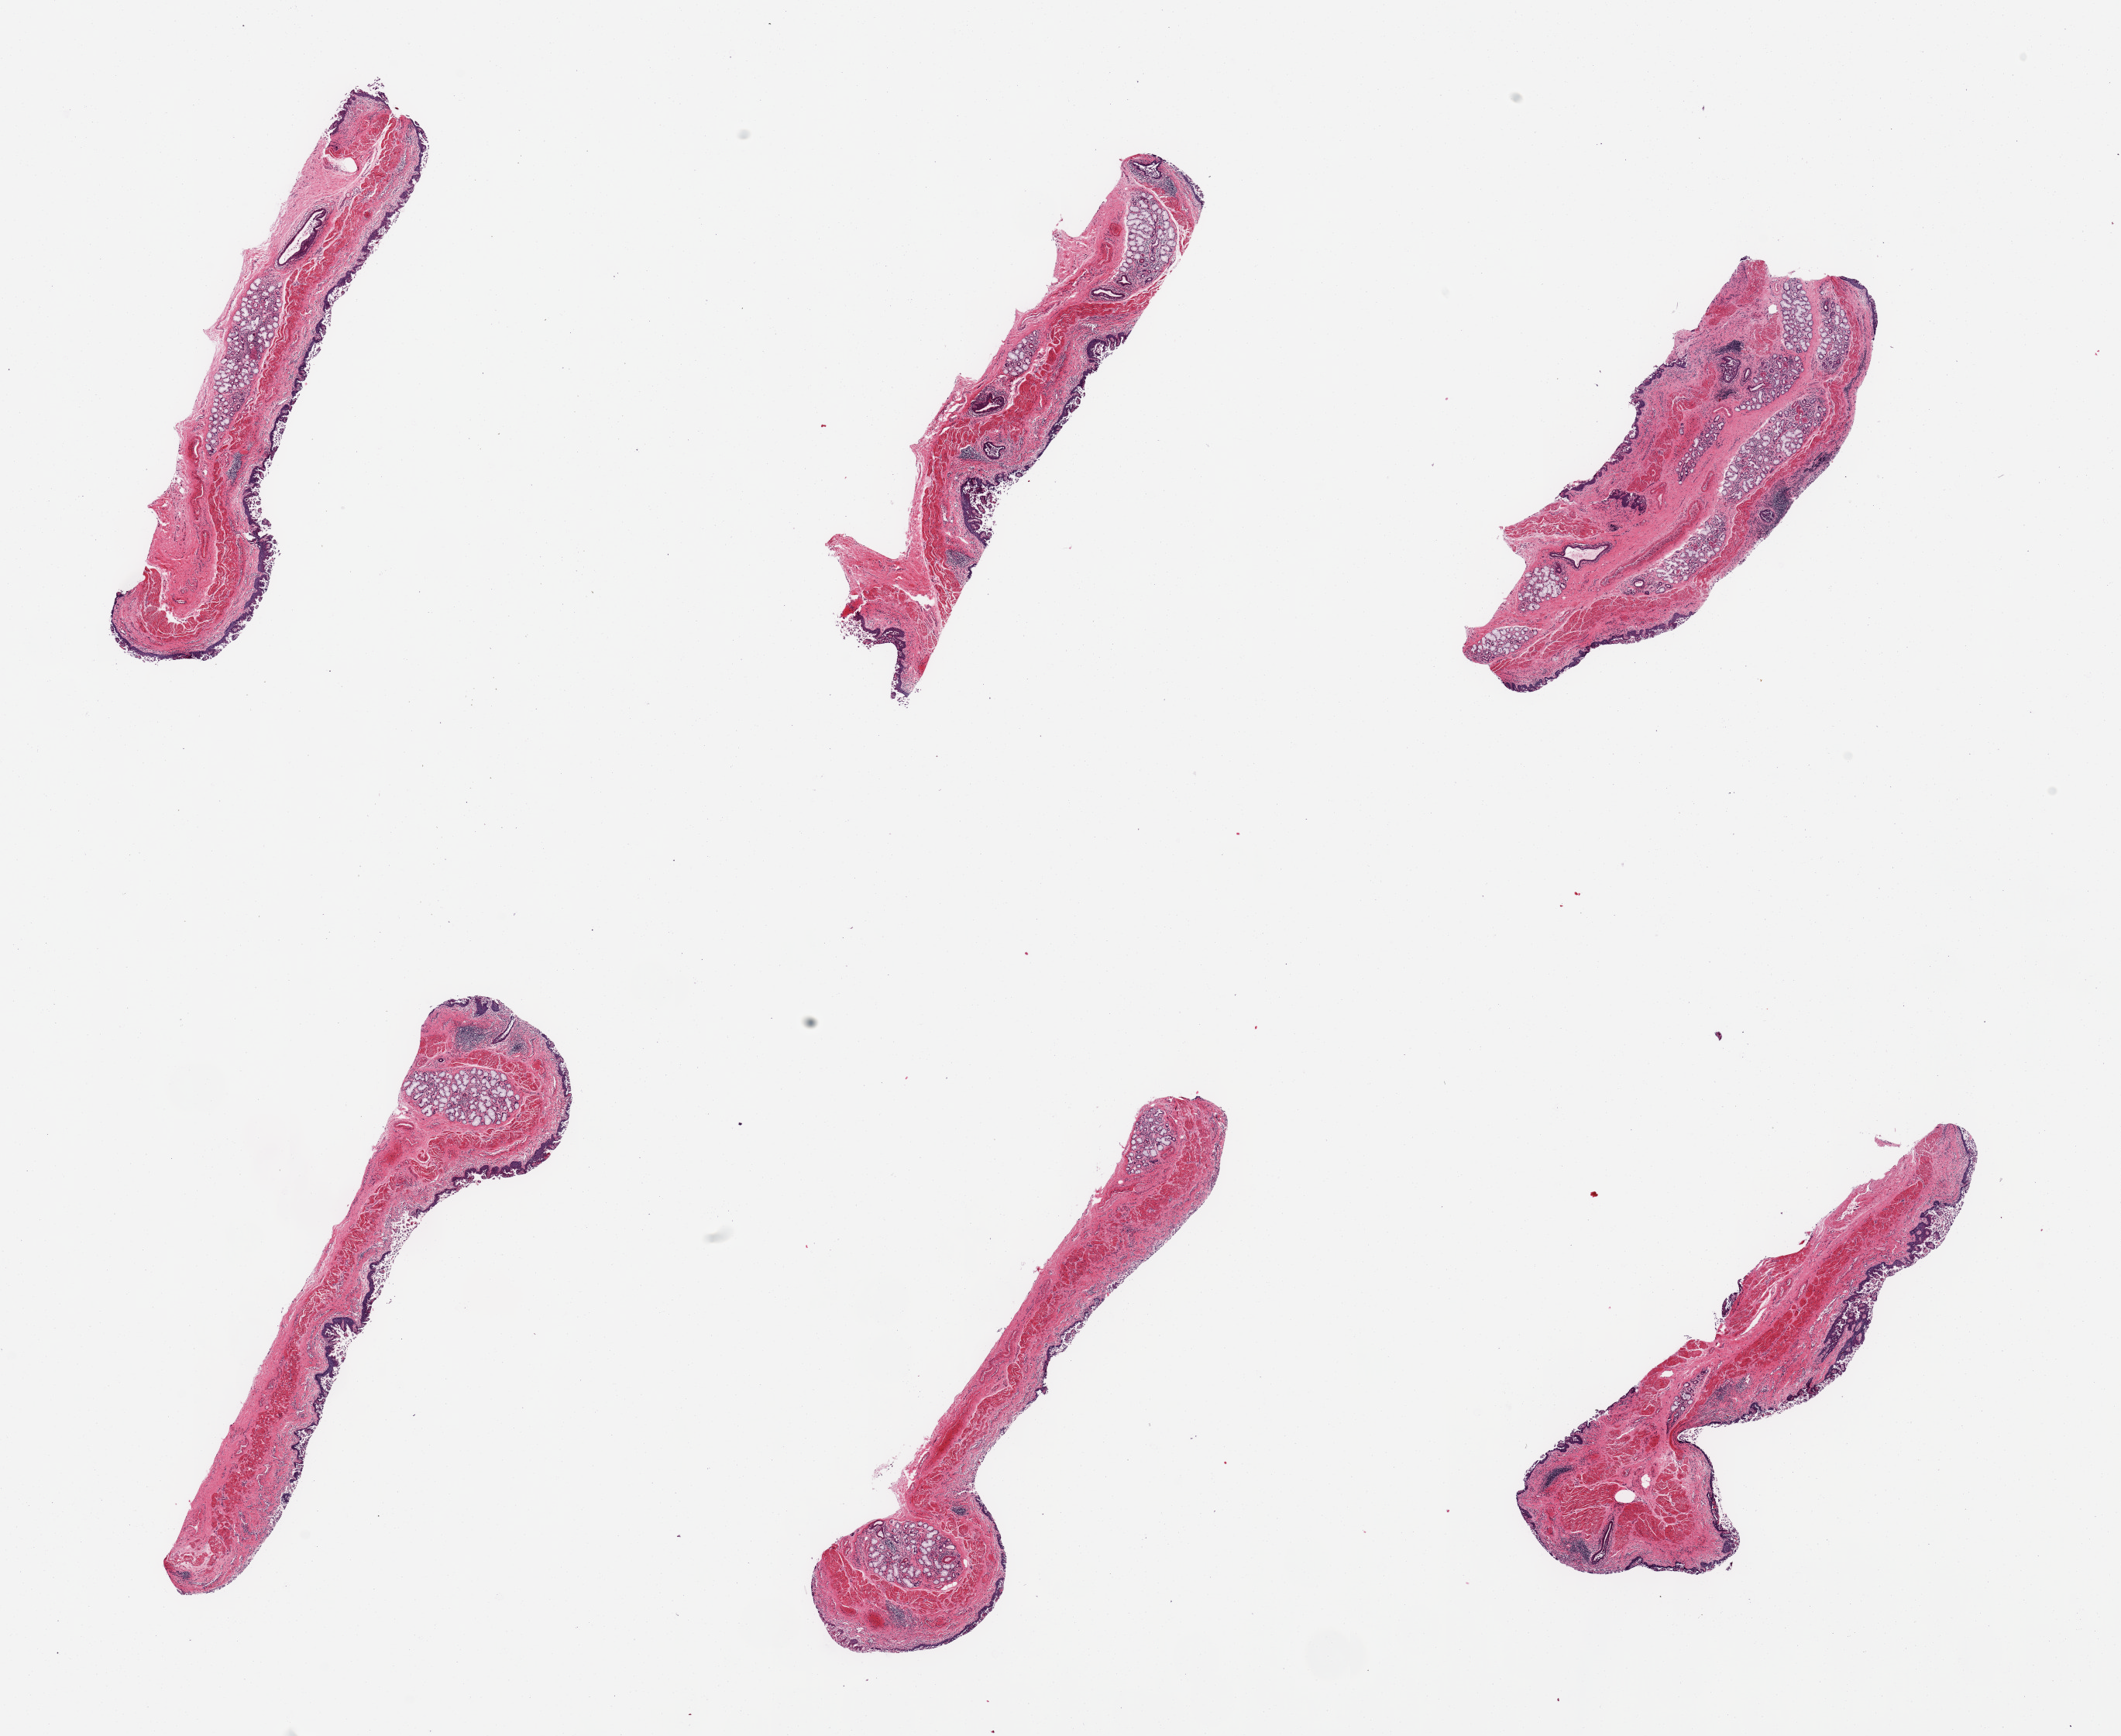
Hematoxylin and eosin (H&E) whole-slide image, low-resolution overview of the scanned area, about 21.7 x 17.7 mm, PAXgene-fixed, paraffin-embedded tissue, section of esophageal mucous membrane (target tissue), donor tissue sample. Donor sex: male.
Review note (as recorded): 6 pieces, moderately advanced autolysis with sloughing squamous mucosa up to ~0.2mm, numerous submucosal mucus glands, fairly well preserved.